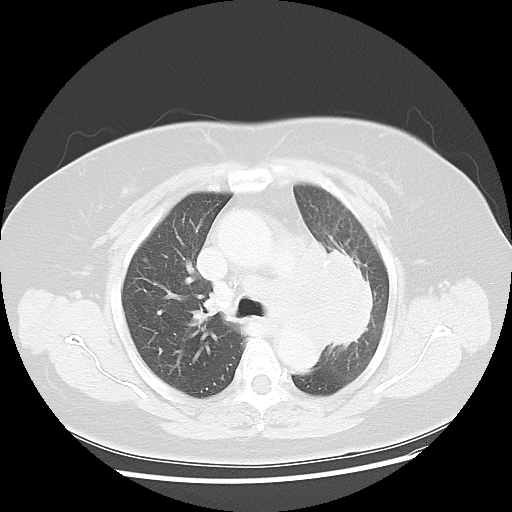
Chest CT, one axial slice. Position 32 of 49 along the scan axis. Lung window (W 1500 / L -600 HU). 5 mm slice thickness. 512 × 512 image matrix, field of view 374 × 374 mm. Patient: female, 58 years. From the clinical record (not read from this slice): clinical TNM (as recorded): T4 N3 M0; histopathological grade: G3.
Annotated regions visible in this slice (rectangle marked by the reading radiologist):
- lung tumour (recorded histology: small cell carcinoma): bounding box (x1, y1, x2, y2) in pixels: (277, 218, 378, 354)